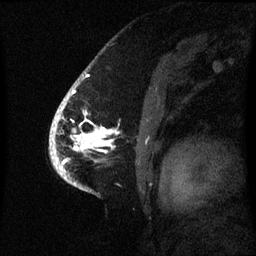
Breast MRI (dynamic contrast-enhanced), one sagittal slice. Slice 47 of 60 in the series (ordered by position). Dynamic contrast-enhanced series, image 2 of 3 at this slice position (ordered by acquisition). 1.5 T. TE 4.2 ms, TR 8.4 ms. 2.1 mm slice thickness. 256 × 256 image matrix, field of view 220 × 220 mm. Patient: female, 53 years. Case-level facts recorded for this patient, not image findings: setting: breast cancer imaged before/during neoadjuvant chemotherapy; receptor status: HR-positive, HER2-negative.
Structures marked on this image (semi-automatically segmented with operator editing):
- analysis volume of interest (the breast-tissue region the enhancement analysis was run in; not a lesion): box from (x=52, y=90) to (x=119, y=171) px
- tumour enhancement mask (voxels above the 70 % enhancement threshold inside the analysis volume of interest): (x=55, y=94)–(x=110, y=171)